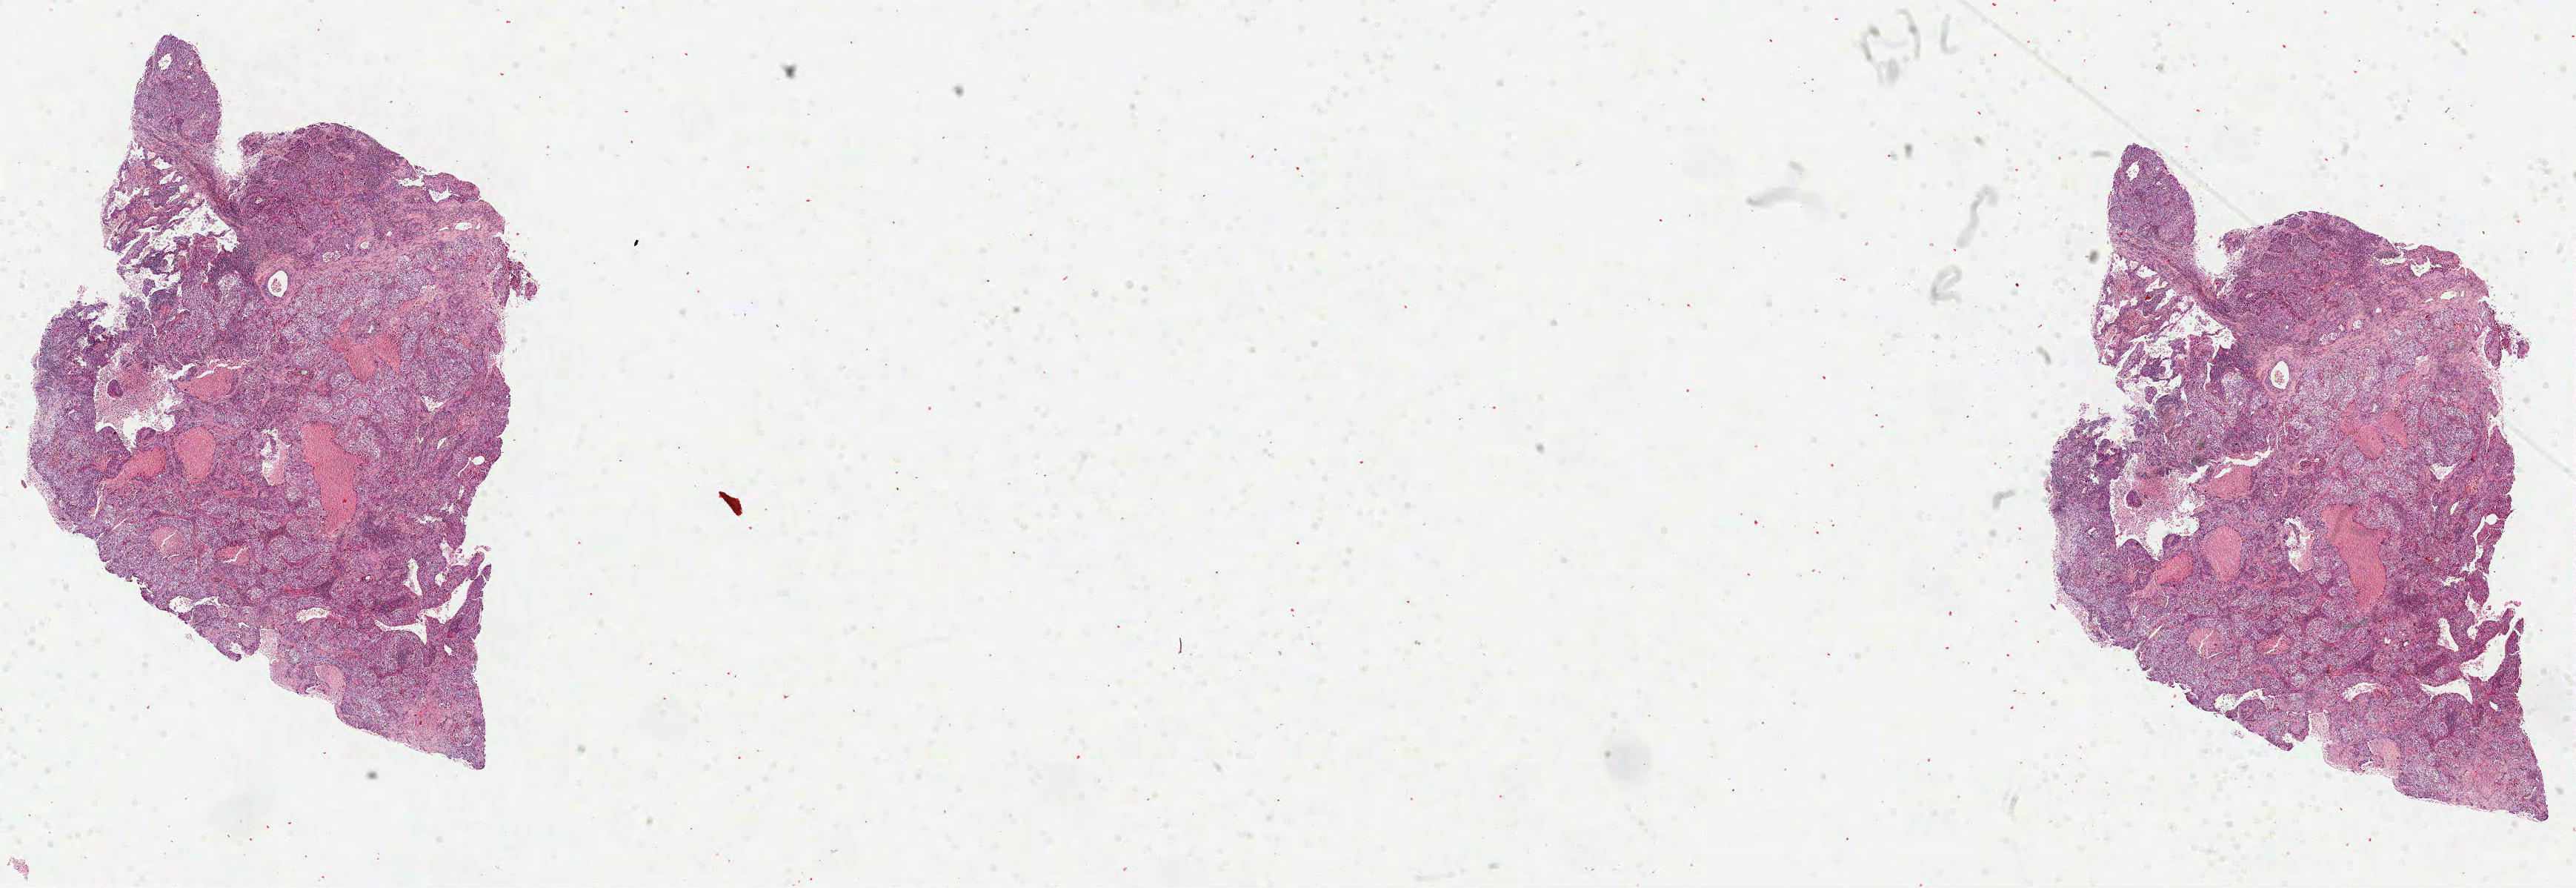
Whole-slide histology image, H&E-stained — a low-resolution overview of the entire scanned area, about 28.0 x 9.7 mm (acquisition: 40x scan), FFPE section, lung, primary tumour sample. Female patient; age at initial diagnosis 59 years.
- diagnosis: Squamous cell carcinoma, NOS
- AJCC pathologic stage: IA
- TNM: T1 N0 M0